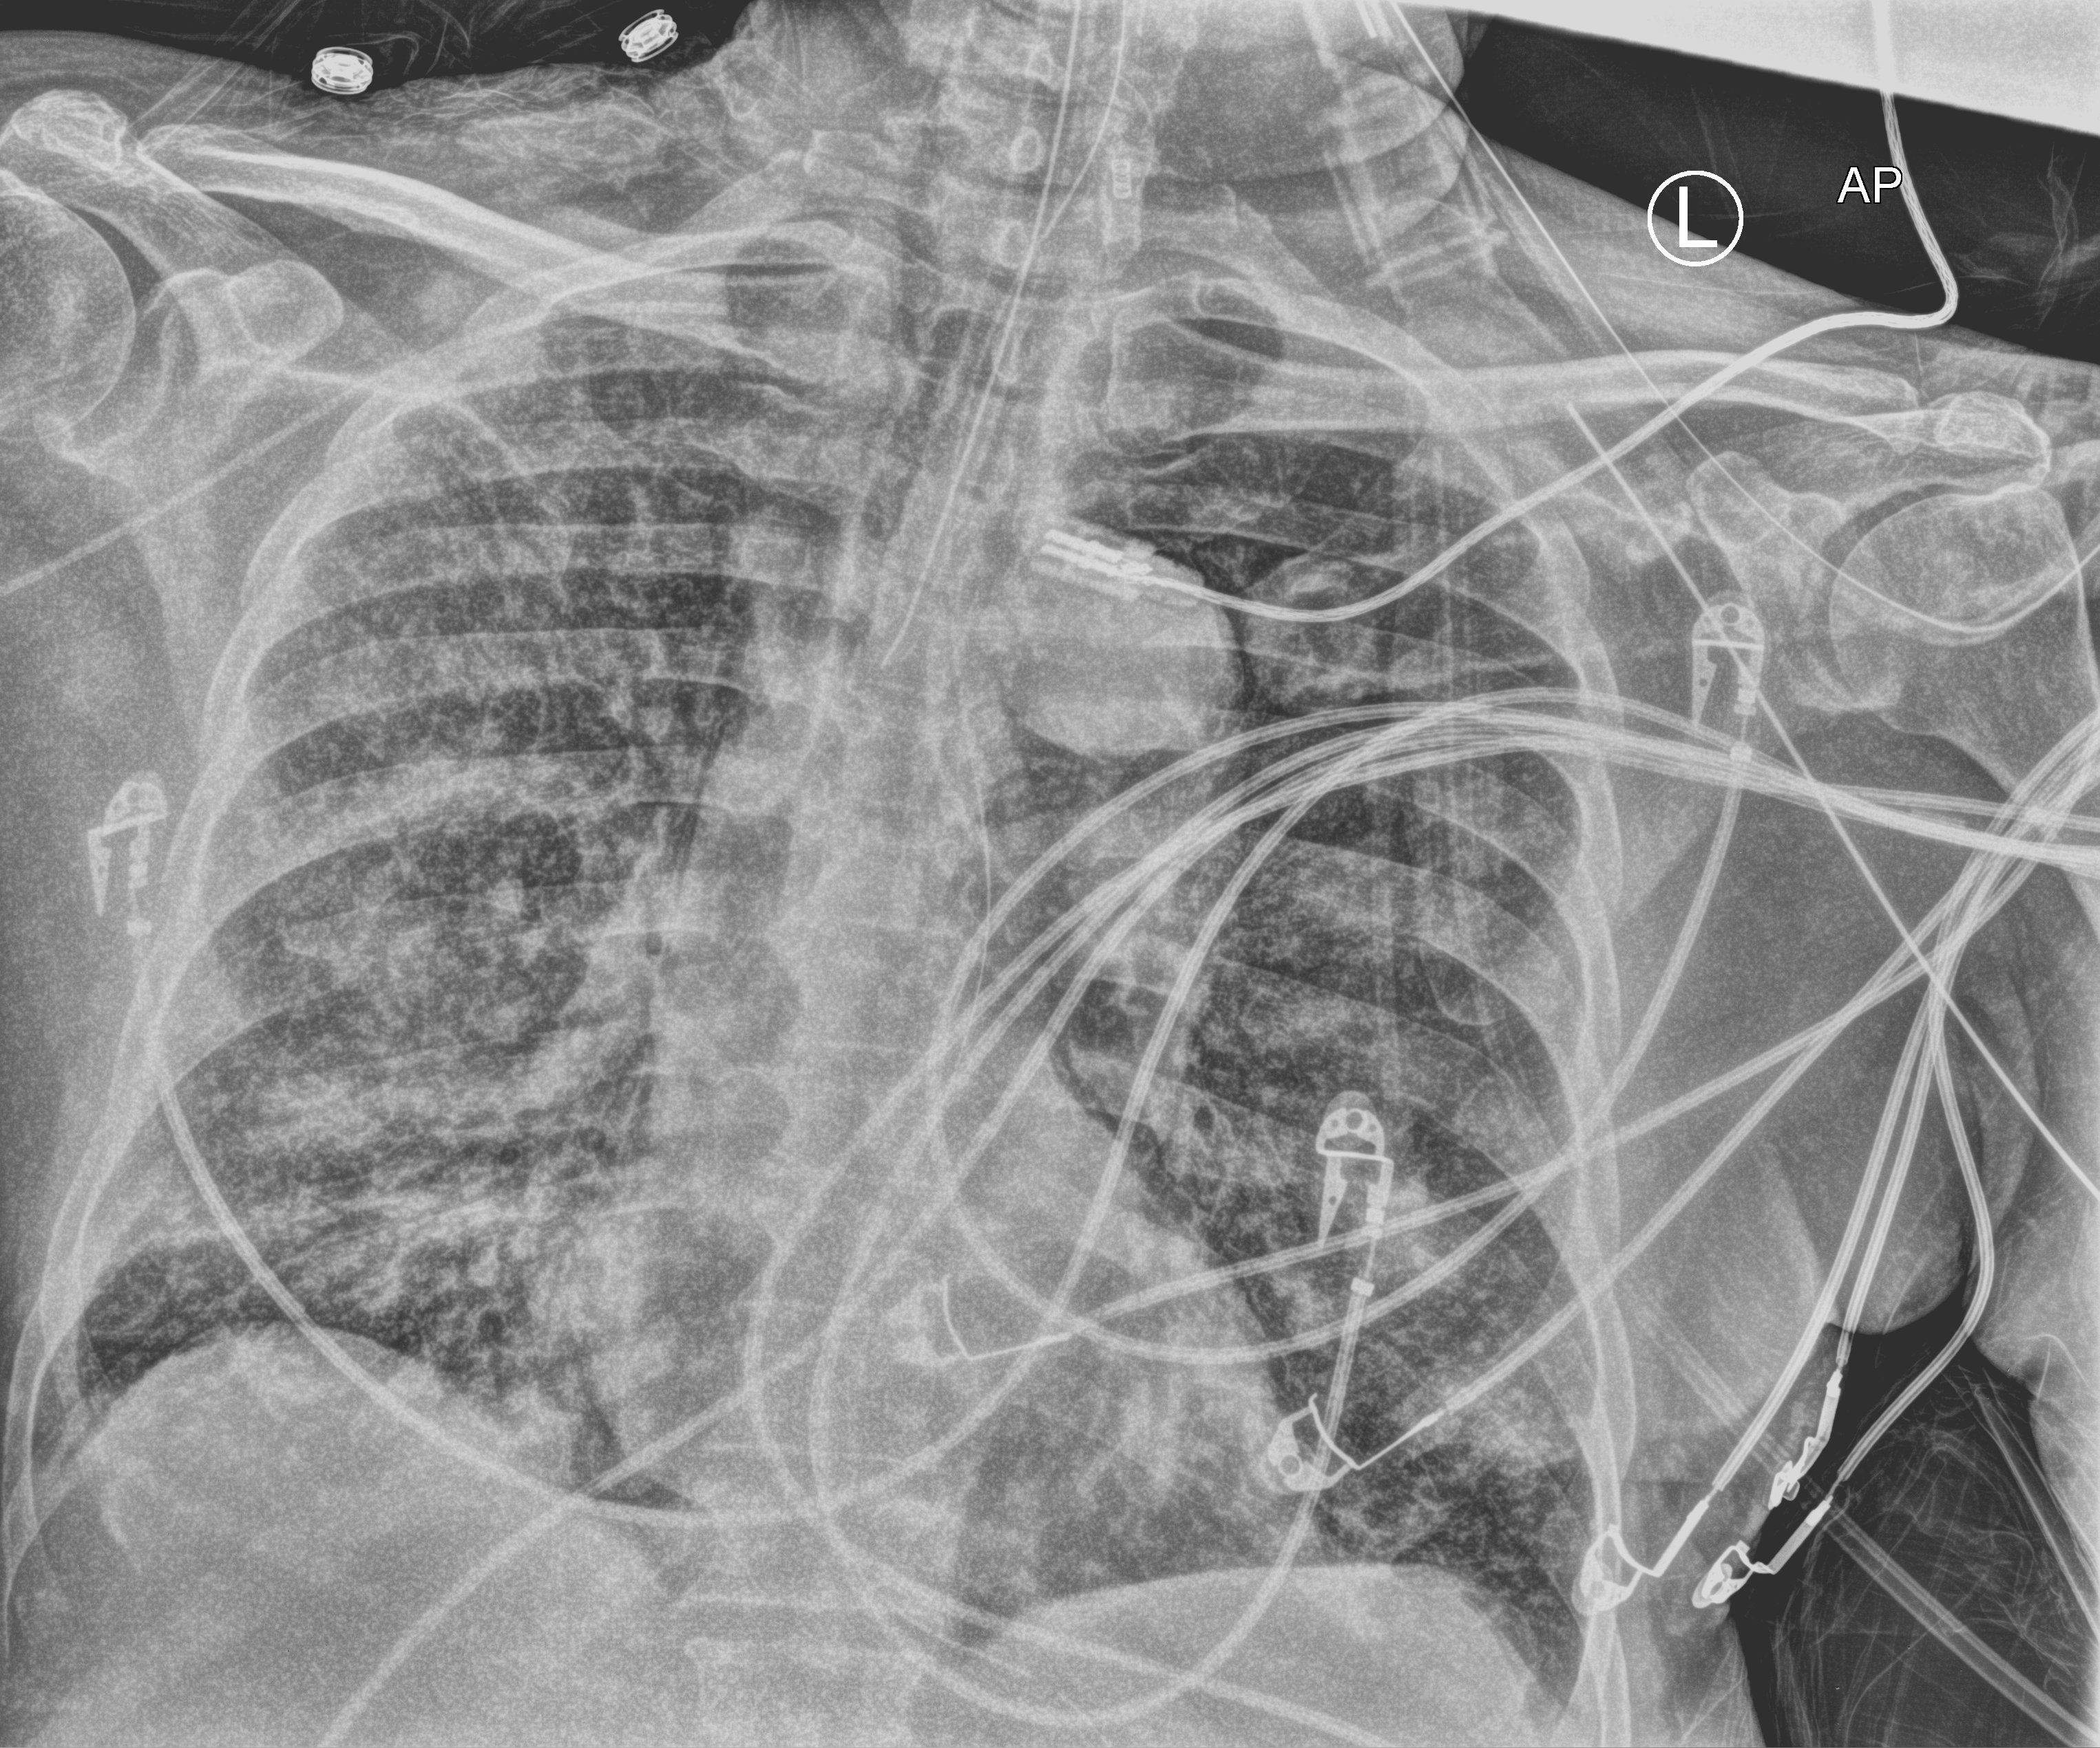
Bedside chest radiograph (computed radiography), anteroposterior (AP) projection. Male patient hospitalised with COVID-19, age 60–74 years.
From the hospital-stay record, not from the radiograph (when in the stay this image was taken is not recorded): chronic kidney disease (admission record): no; mechanically ventilated during this hospital stay: yes; admitted to intensive care during this hospital stay: yes.